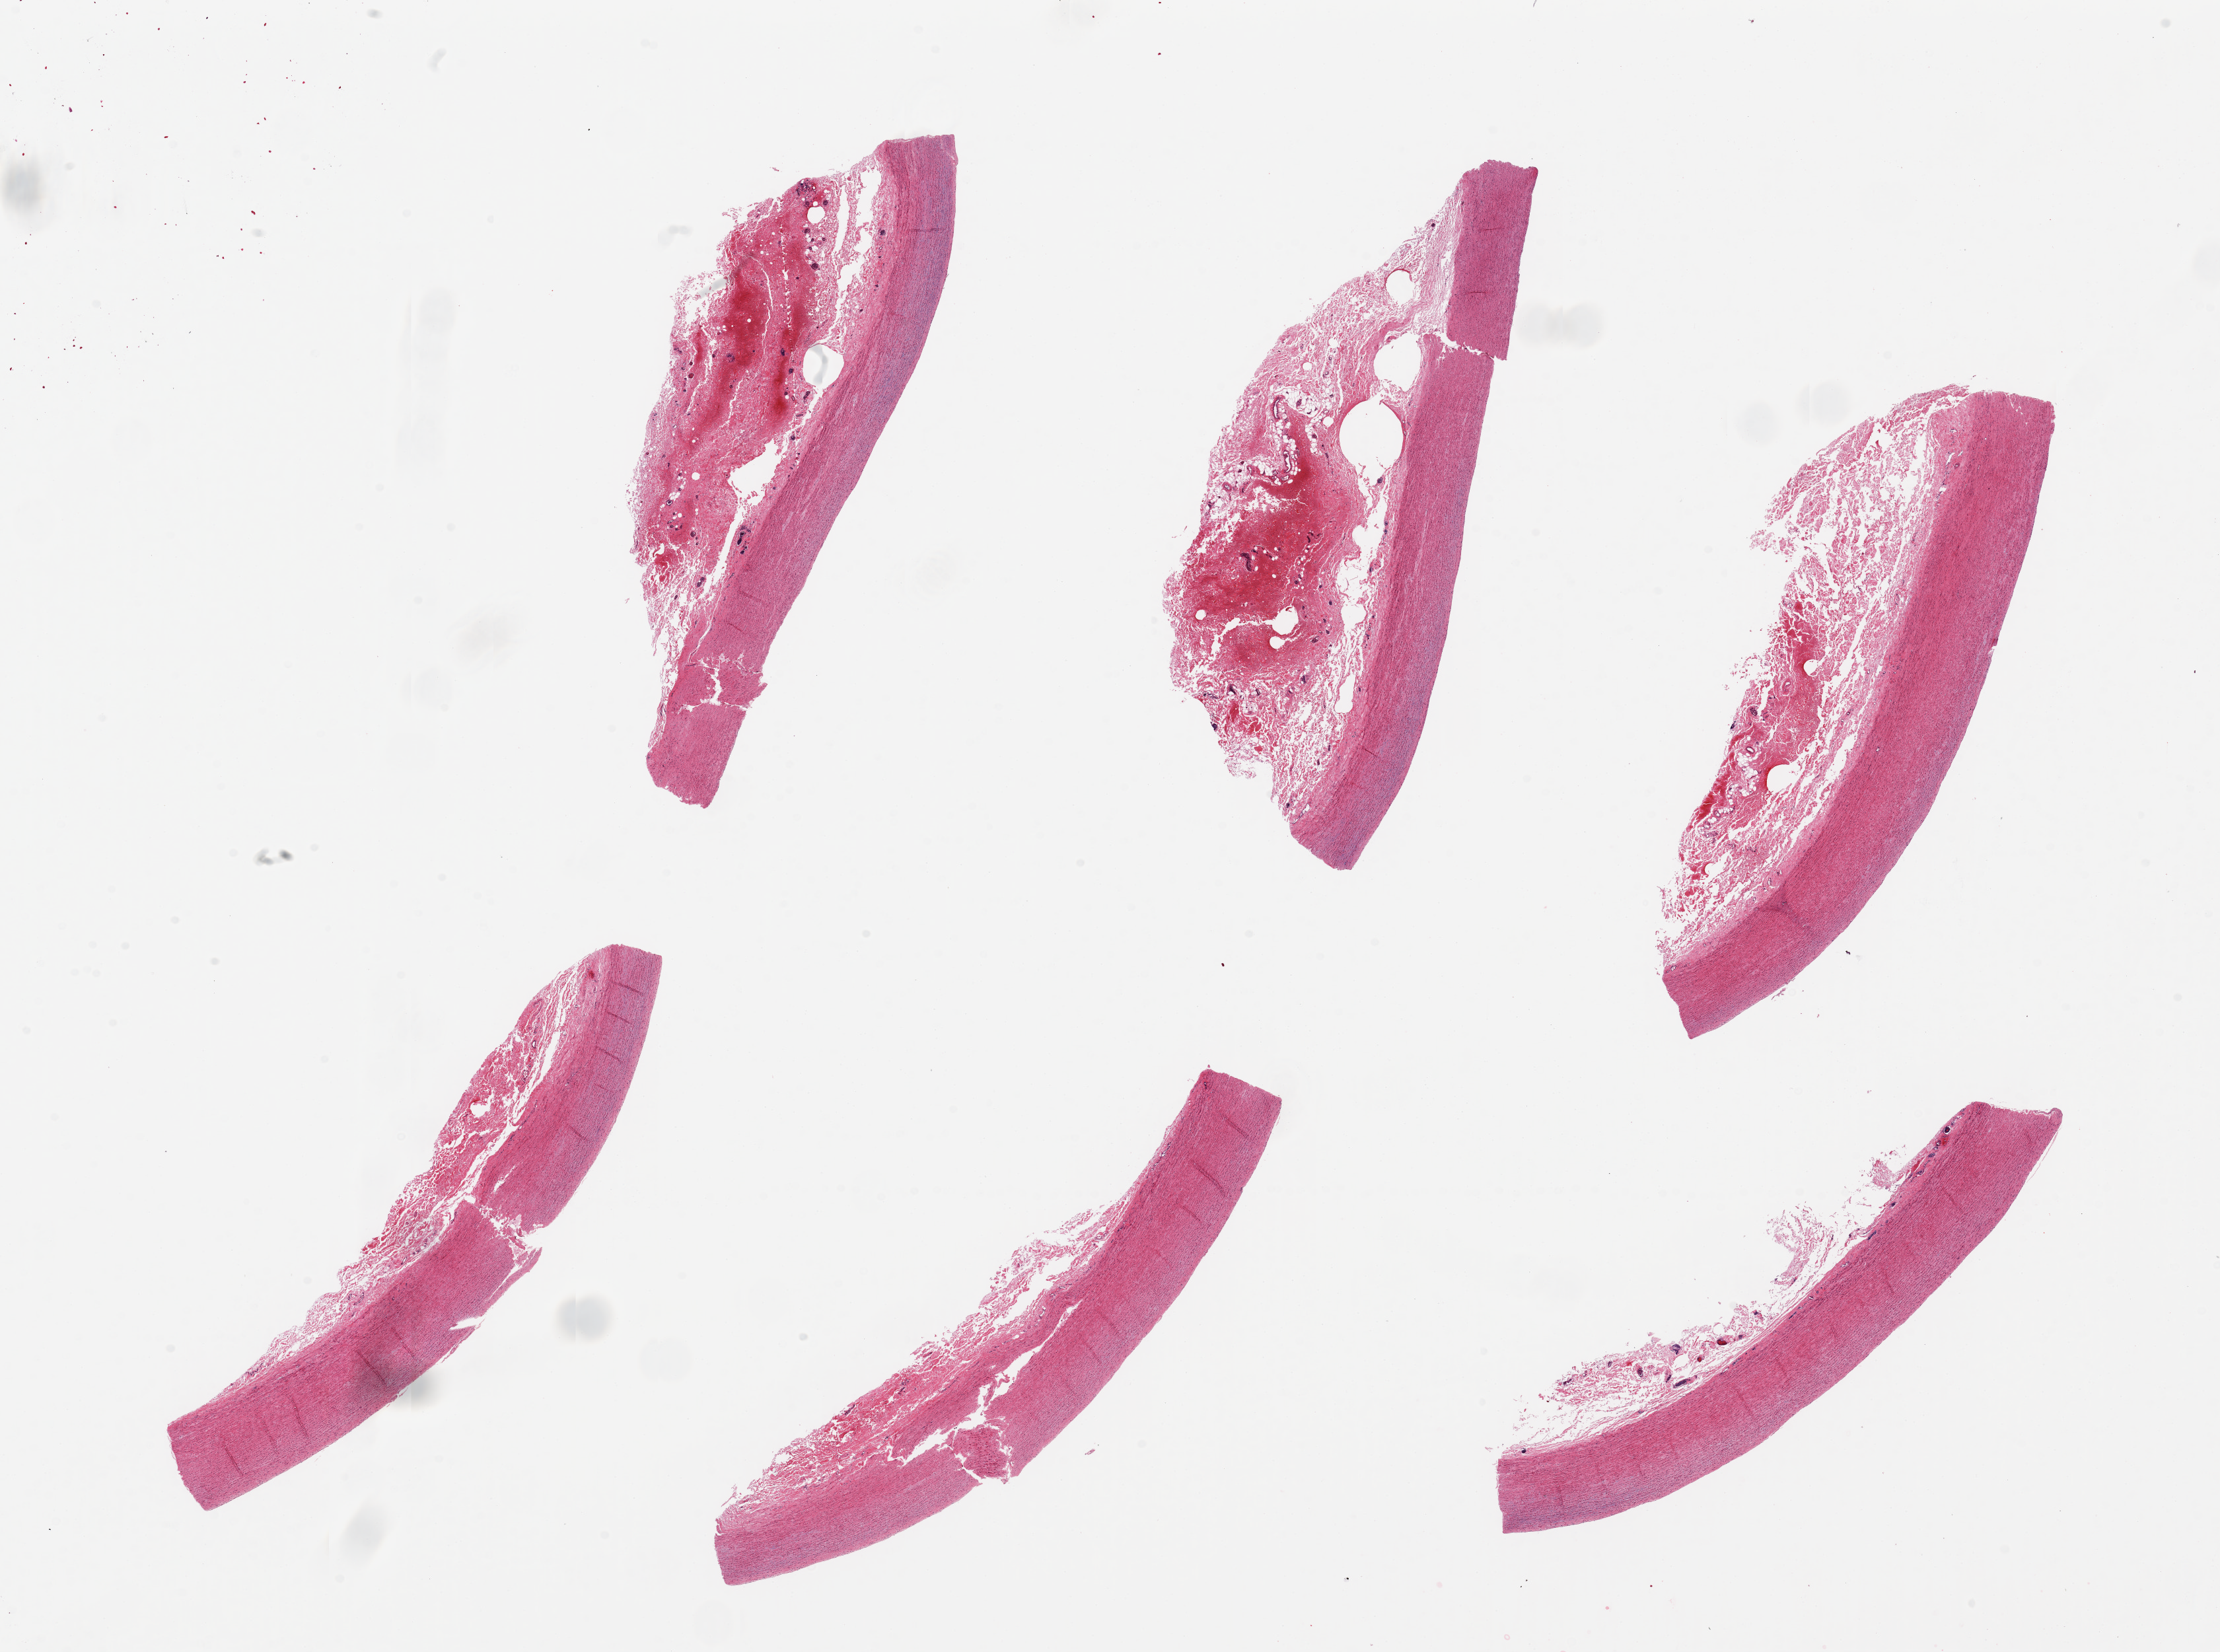
Digitized haematoxylin and eosin-stained section — shown as a low-resolution overview of the whole scanned area (about 26.6 x 19.8 mm, slide scanned at 20x). PAXgene-fixed paraffin-embedded (PFPE) section. Target tissue: aorta. Tissue donor sample. Donor sex: male.
Pathologist's review note for this sample: 6 pieces ~9x1mm, 4 of 6 have adherent fat/vasa vasorum up to 2mm thick.